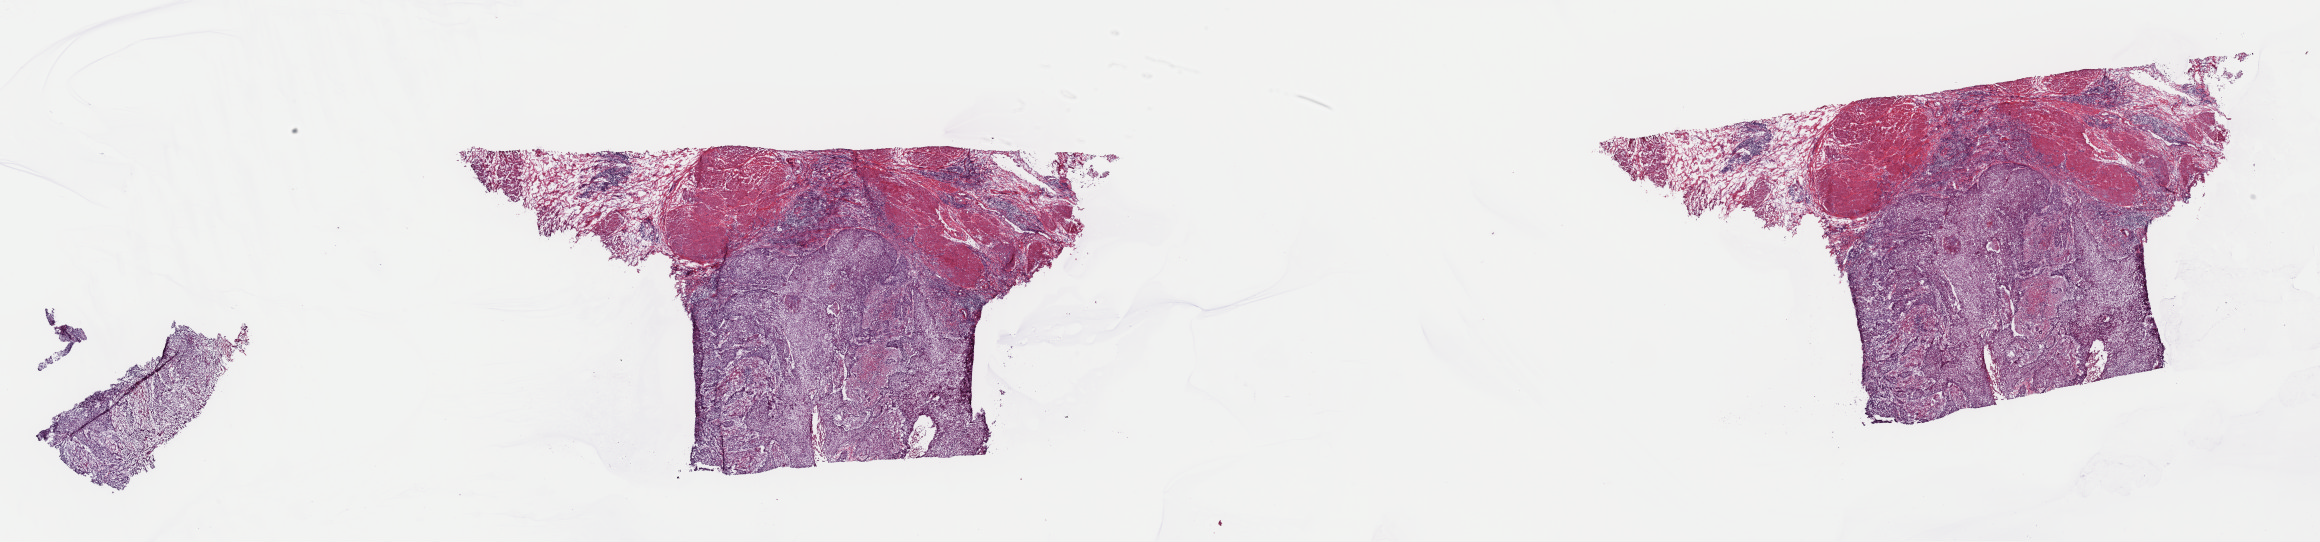
Whole-slide histology image, Hematoxylin and eosin (H&E) stained — low-resolution overview of the scanned area, about 36.7 x 8.6 mm (from a 40x scan). Frozen section. Sample: primary tumour, bladder. Female, age 76 years at initial diagnosis. Histologic grade: high grade. Pathologist review of this section (percent, as recorded): tumour cells 30%, tumour nuclei 60%, normal cells 0%, stromal cells 67%, necrosis 3%. Inflammatory infiltration, as recorded: lymphocyte infiltration 22%, monocyte infiltration 2%, neutrophil infiltration 4%.
* pathologic diagnosis: Transitional cell carcinoma (lateral wall of bladder)
* lymph nodes positive (case pathology): 0 of 47 examined
* AJCC pathologic stage: II (7th edition)